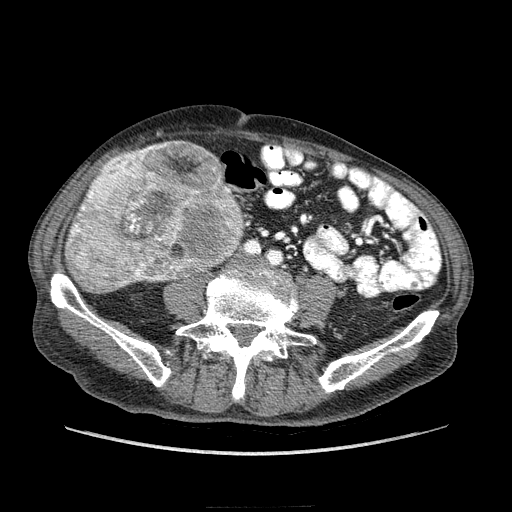
Contrast-enhanced abdominal CT (liver protocol), one axial slice; position 39 of 218 along the scan axis; reconstruction kernel STANDARD; soft-tissue window (W 400 / L 40 HU); 512 × 512 image matrix, field of view 380 × 380 mm. From the clinical record (not read from this slice): diagnosis: hepatocellular carcinoma (patient treated with transarterial chemoembolisation; whether this scan precedes or follows treatment is not stated here); TNM stage (as recorded): Stage-IIIA; Child-Pugh class: A; tumour differentiation: well differentiated; tumour size: 20 cm.
Annotated regions visible in this slice (semi-automatically segmented with operator editing):
- liver parenchyma outside the tumour (the mass and vessels are separate outlines, so this box may not span the whole liver): box from (x=70, y=146) to (x=148, y=282) px
- mass: (x=64, y=138)–(x=244, y=293)